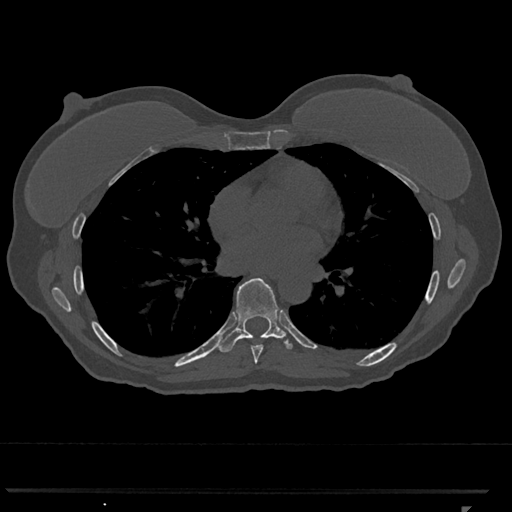
CT including the spine, one axial slice. Reconstruction kernel Br40s/3. Bone window (W 1800 / L 400 HU). 0.5 mm slice thickness. 512 × 512 image matrix, field of view 380 × 380 mm. Female patient, age 62 years. Case-level facts recorded for this patient, not image findings: primary cancer: renal.
Annotated regions visible in this slice (semi-automatically segmented with operator editing):
- T7 vertebra: bounding box [x1, y1, x2, y2] px = [251, 345, 264, 364]
- T8 vertebra: [219, 278, 293, 352]